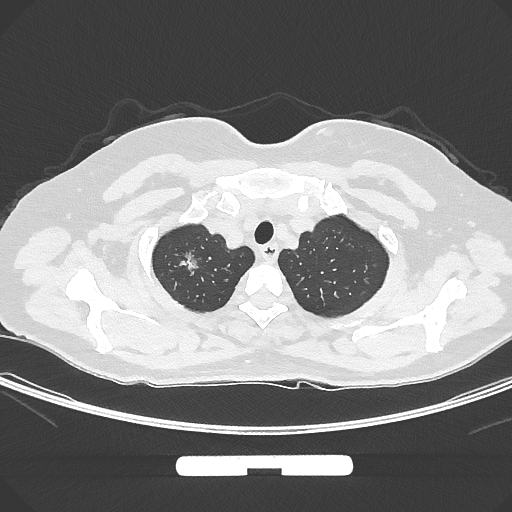
Chest CT, one axial slice; slice 260 of 294 in the series (ordered by position); reconstruction kernel IMR1,SharpPlus; 120 kVp; lung window (W 1500 / L -600 HU); 1 mm slice thickness; 512 × 512 image matrix. Patient: female, 58 years. From the clinical record (not read from this slice): clinical TNM (as recorded): T1b N0 M0.
Annotated regions visible in this slice (bounding box drawn by a radiologist):
- lung tumour (recorded histology: adenocarcinoma): bounding box [x1, y1, x2, y2] px = [174, 245, 201, 286]